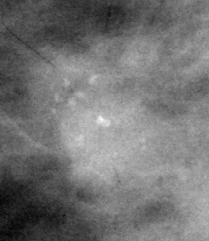
Crop from a digitized film mammogram around one marked abnormality; right breast; MLO view; BI-RADS breast density category 3 (scale 1–4).
Finding: calcifications, morphology pleomorphic, distribution clustered; BI-RADS assessment category 4; pathology (as recorded): malignant.